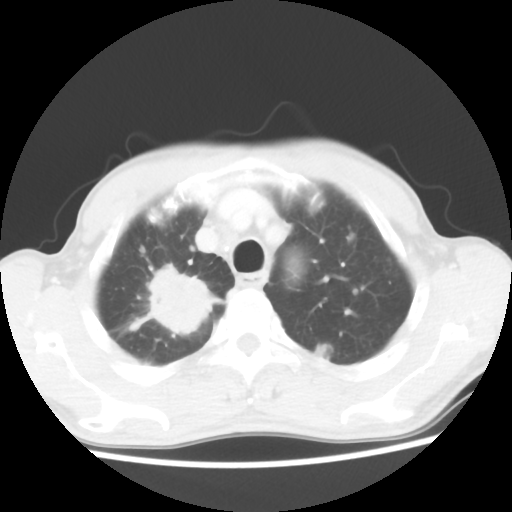
Chest CT, one axial slice. Position 43 of 52 along the scan axis. Lung window (W 1500 / L -600 HU). 512 × 512 image matrix, field of view 323 × 323 mm. Patient: male, 66 years. Case-level facts recorded for this patient, not image findings: clinical TNM (as recorded): T2 N0 M1a.
Structures marked on this image (rectangle marked by the reading radiologist):
- lung tumour (recorded histology: adenocarcinoma): bounding box [x1, y1, x2, y2] px = [126, 261, 221, 343]